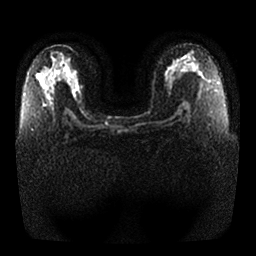
Breast MRI, one axial slice. Position 14 of 25 along the scan axis. Diffusion-weighted series; image 2 of 4 stored at this slice position (different b-values; order by instance number). 1.5 T. 4 mm slice thickness. 256 × 256 image matrix, field of view 350 × 350 mm. Female patient.
Outlined on this slice (expert manual segmentation):
- tumour on diffusion-weighted imaging: bounding box (x1, y1, x2, y2) in pixels: (72, 80, 79, 90)